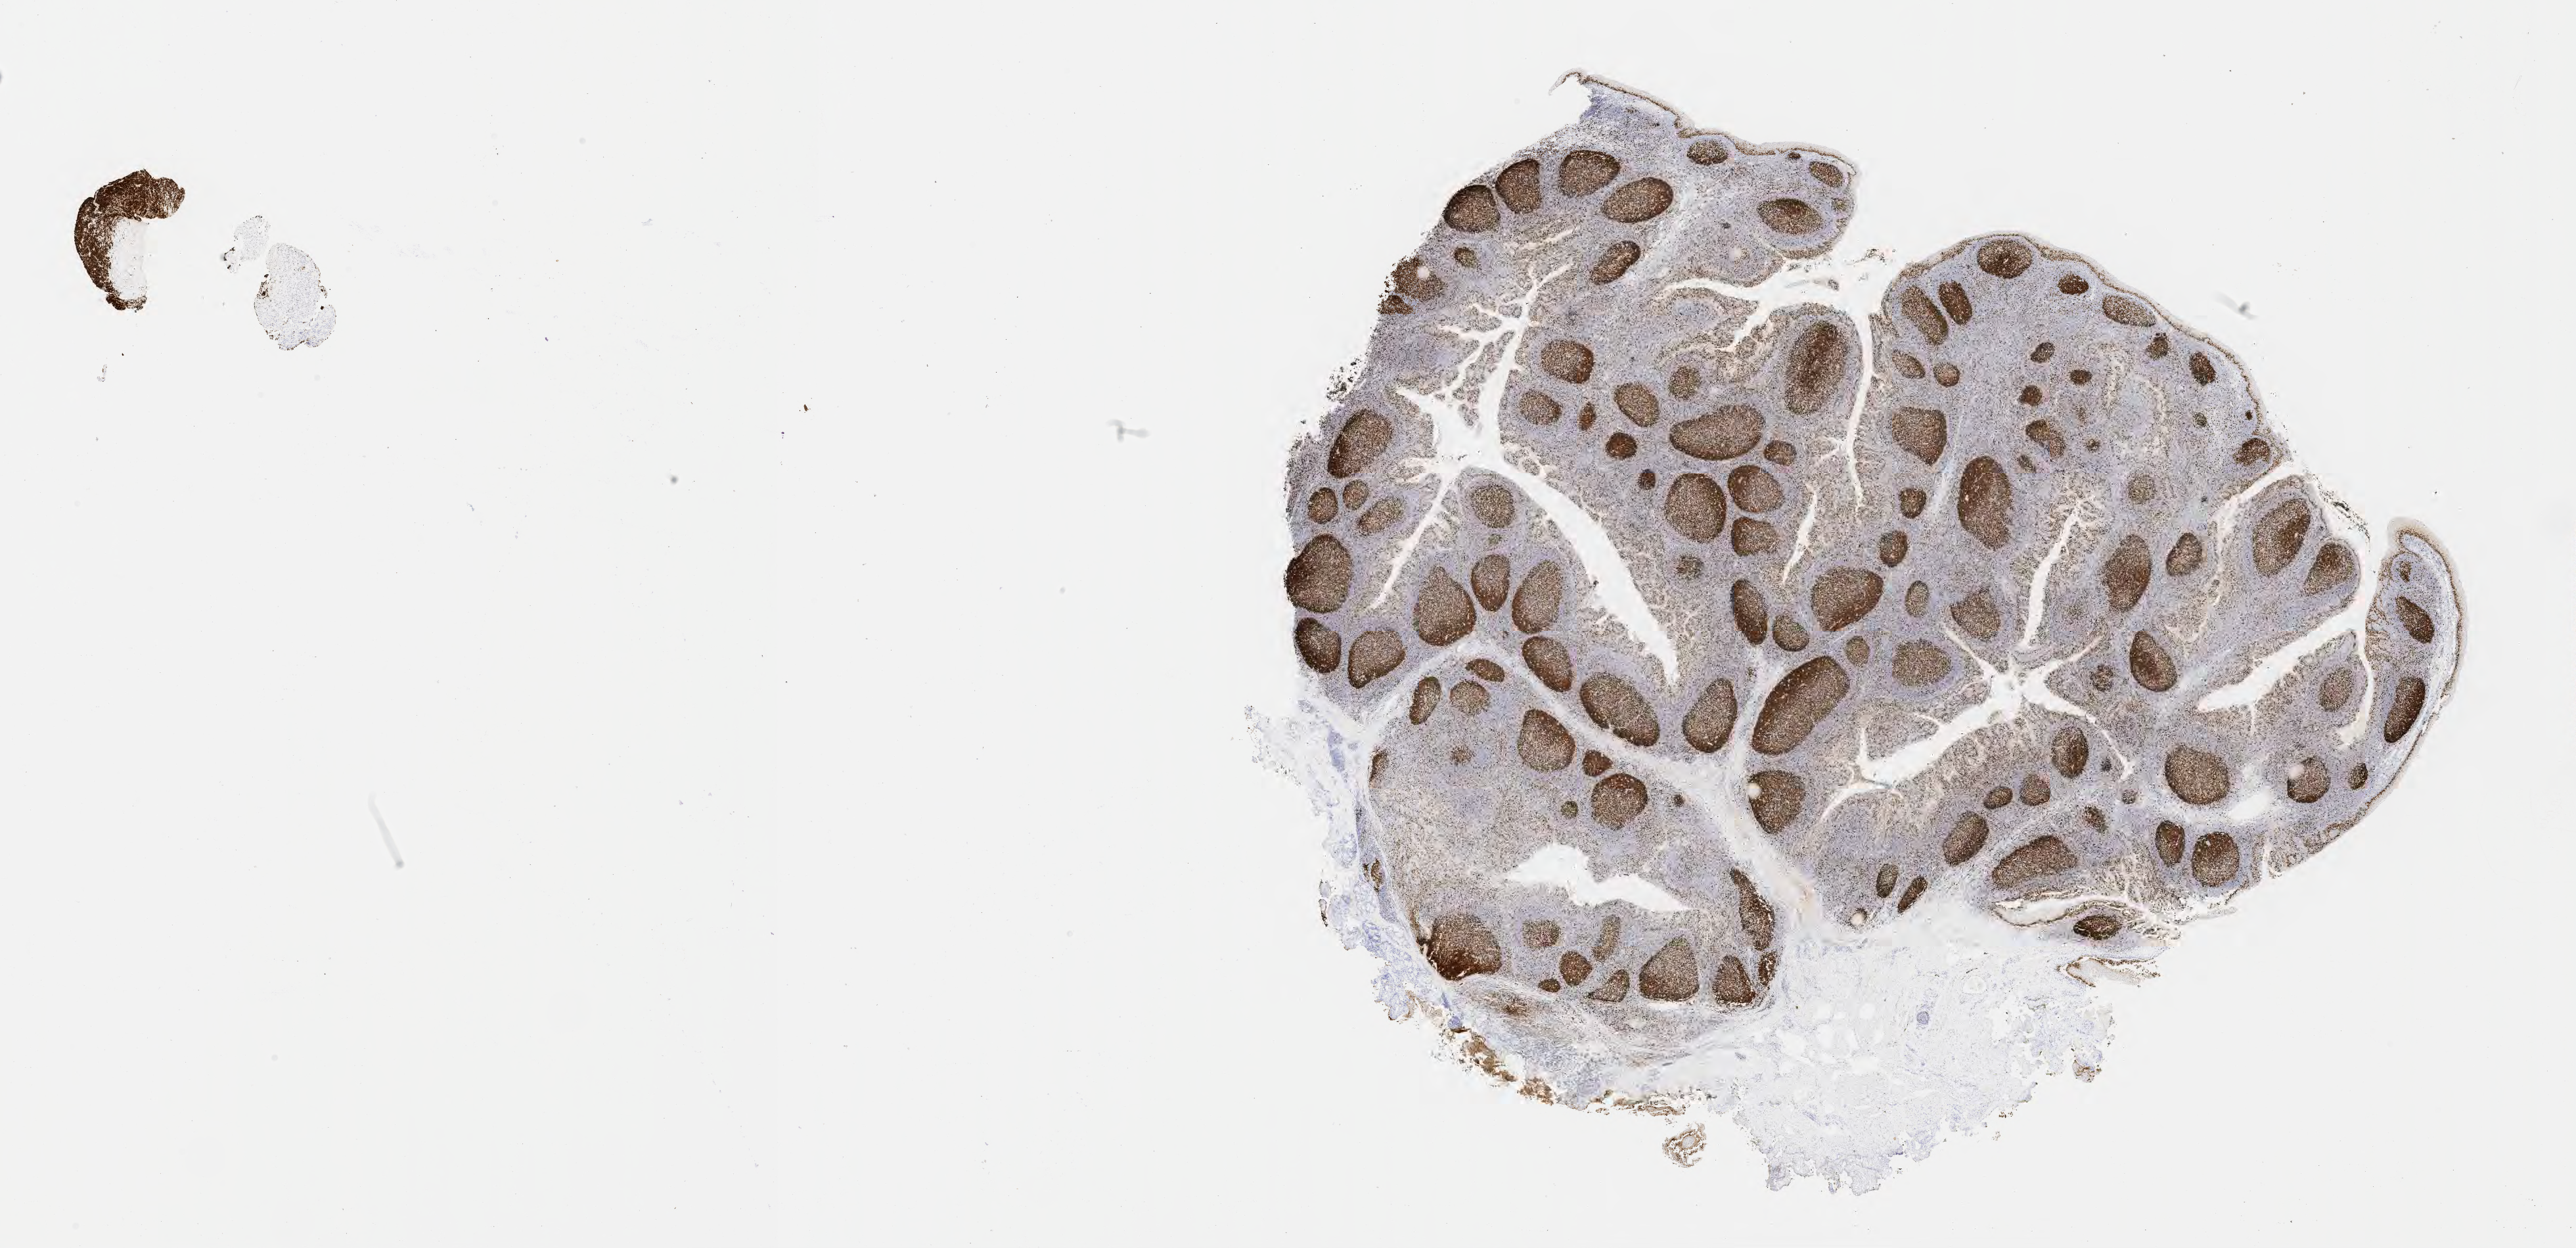
Immunohistochemistry (IHC) whole-slide image stained for Ki-67 — whole scanned area (about 31.7 x 15.3 mm) shown as a low-resolution overview. Specimen: tumor tissue. Anatomic site: abdomen proper. Female, age 6 years at initial diagnosis.
- histologic diagnosis: Diffuse large B-cell lymphoma, NOS